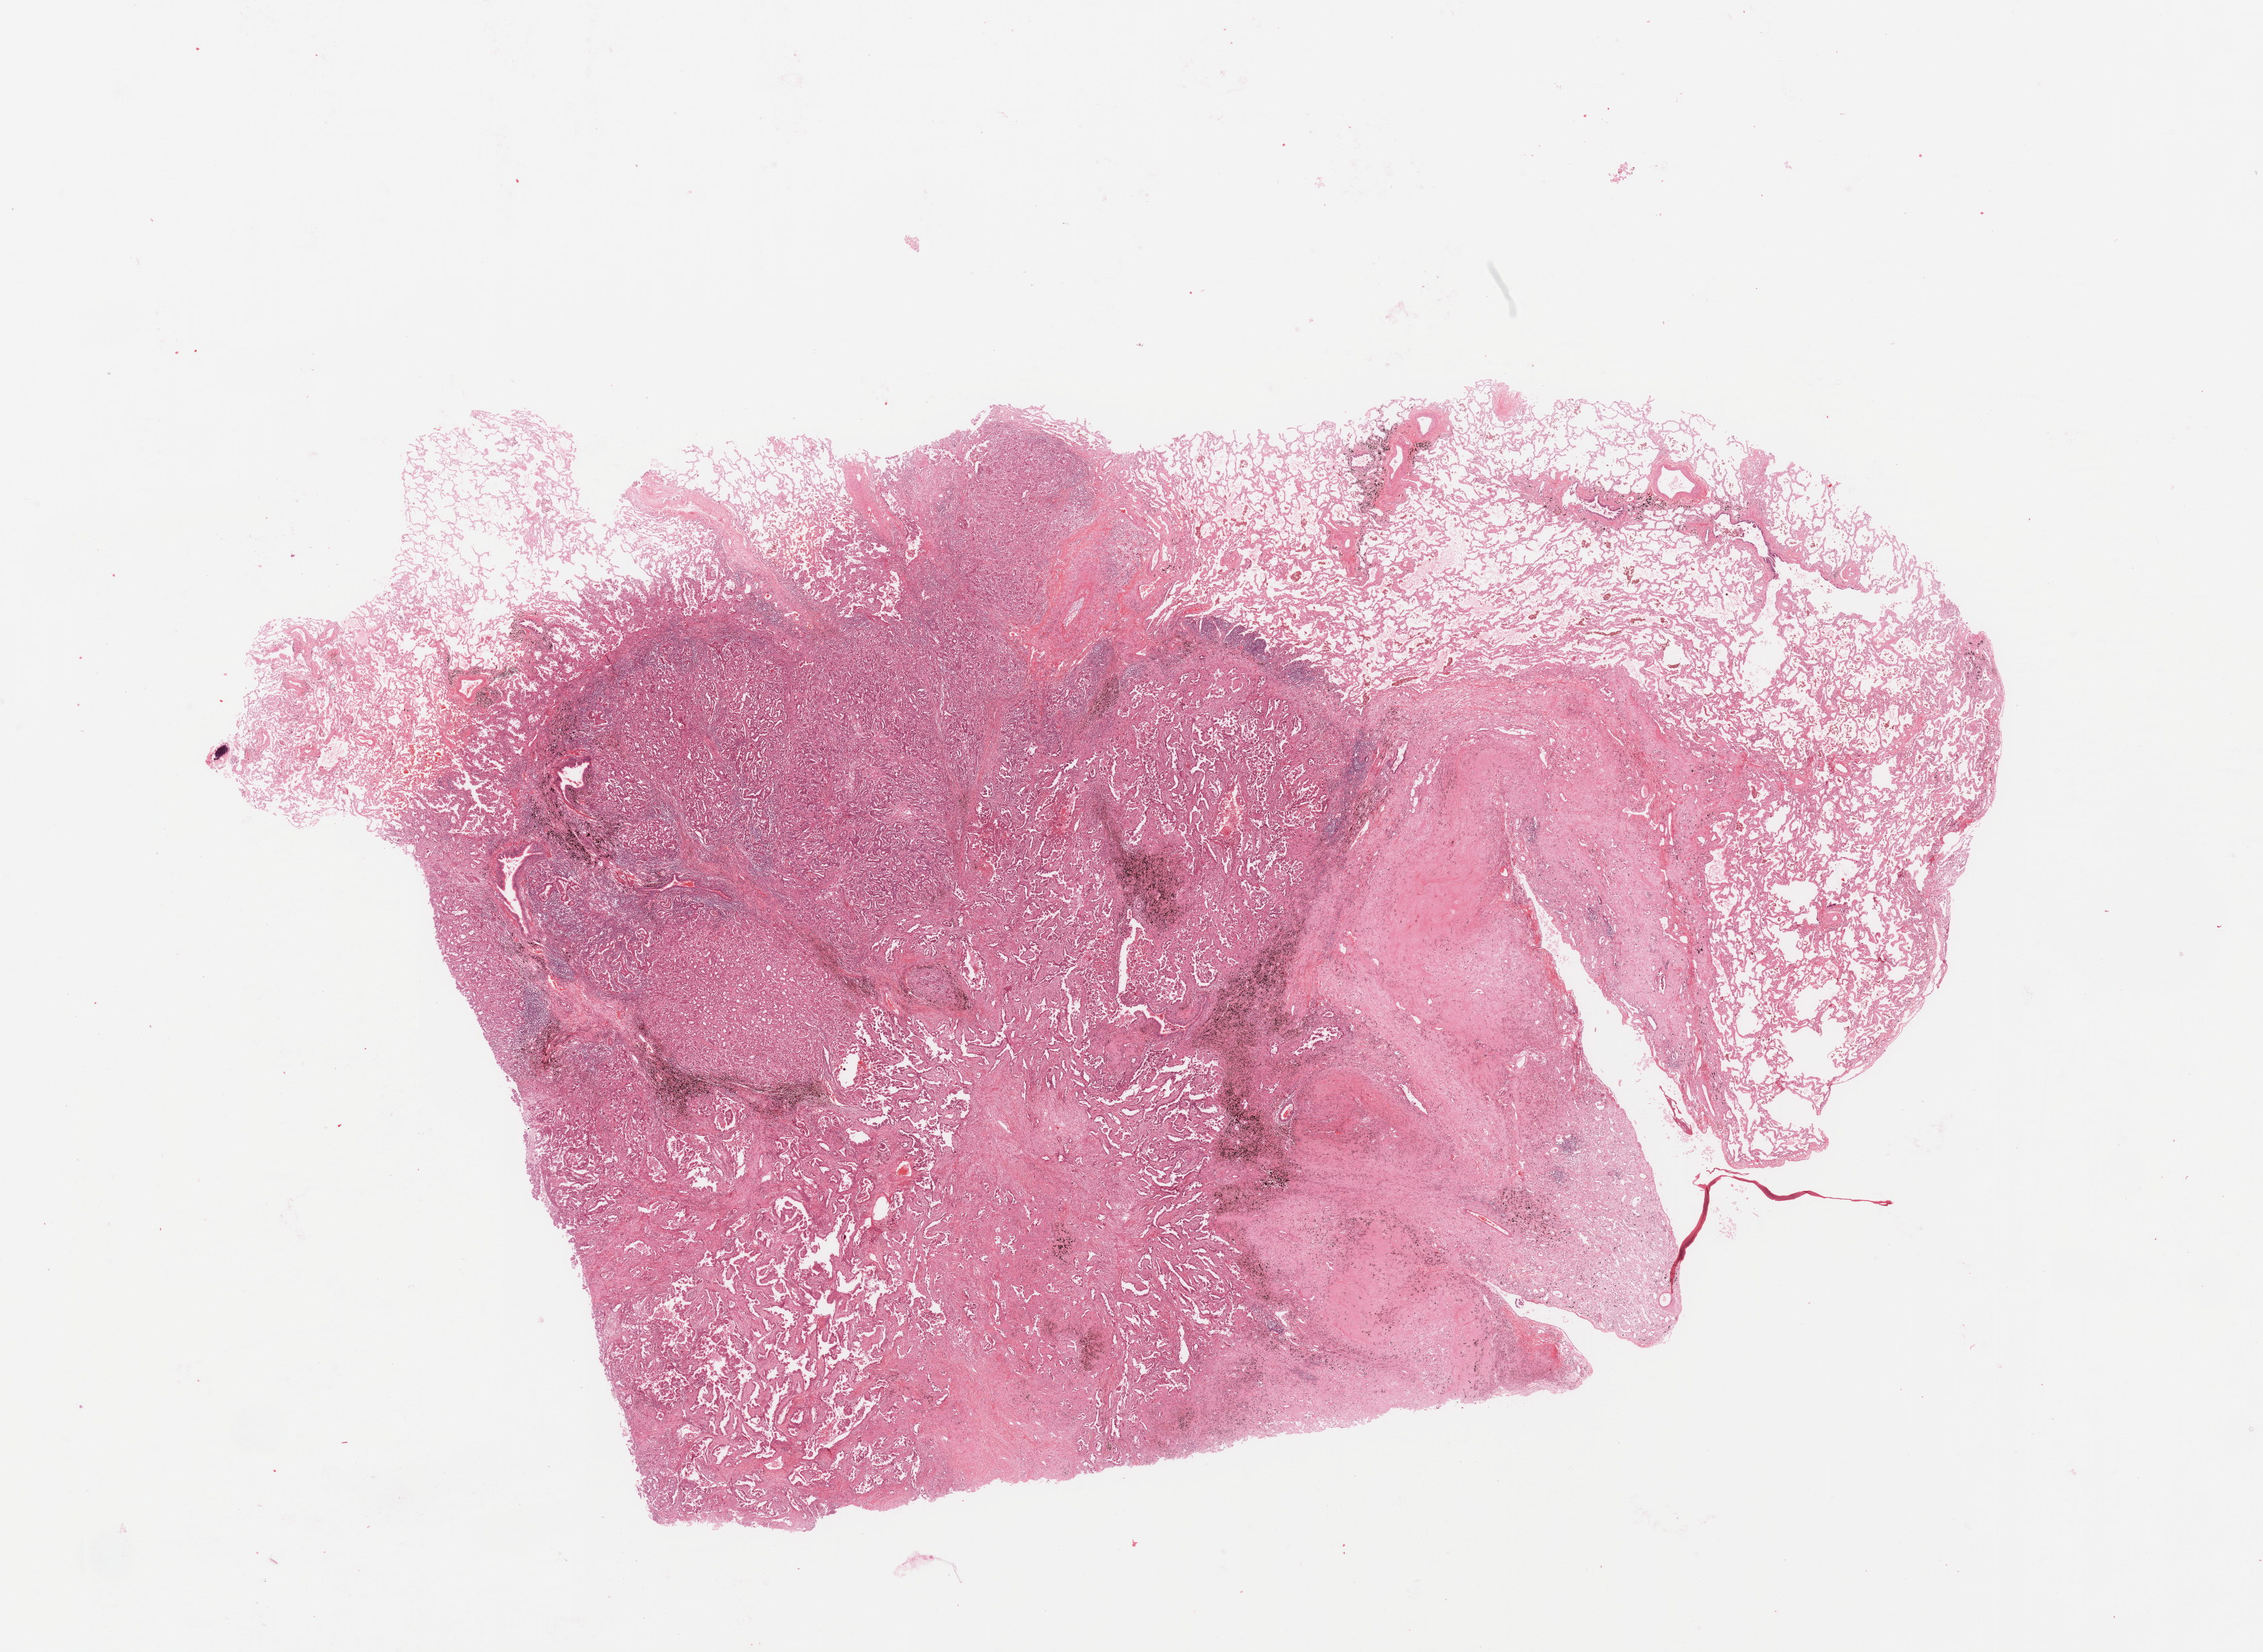
H&E whole-slide image, whole scanned area (about 26.6 x 19.4 mm, from a 20x scan) shown as a low-resolution overview; tumour tissue sample, lung. 67-year-old female patient. Histologic grade: G2 (moderately differentiated).
* diagnosis: Adenocarcinoma, NOS
* AJCC pathologic stage: IIIA